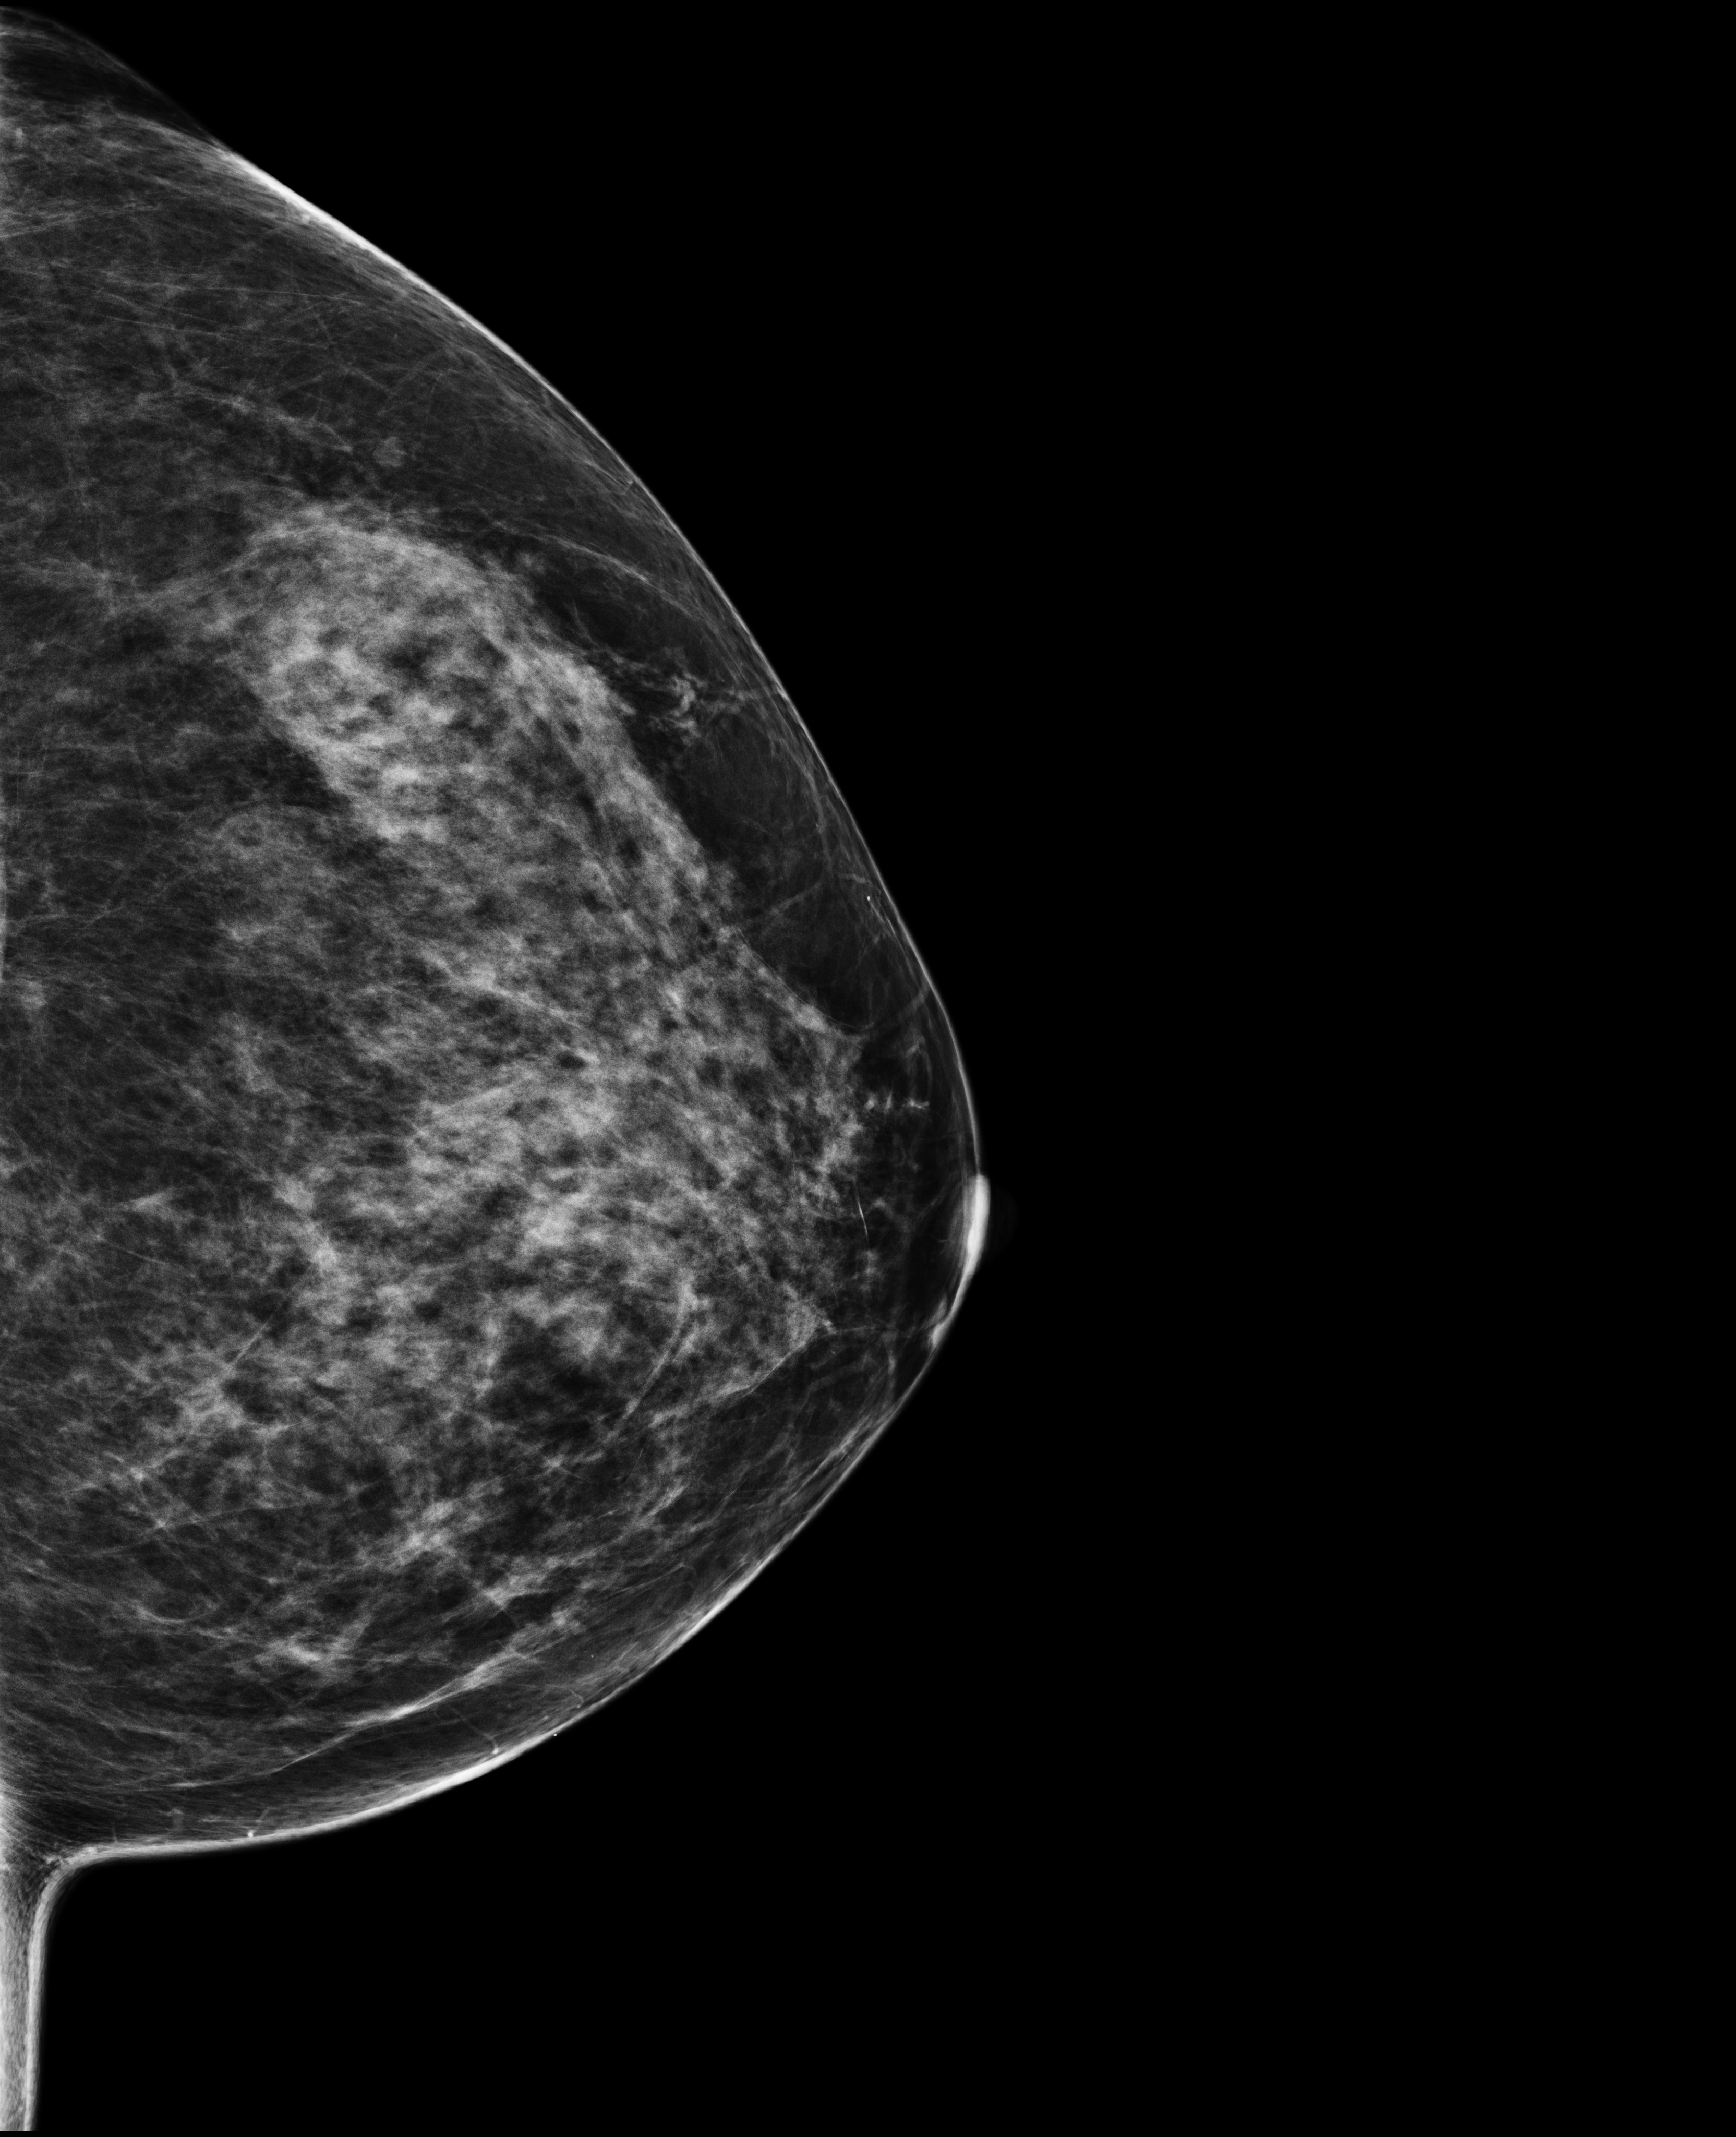
Annual screening mammography examination; compressed breast thickness 74 mm; system: Selenia Dimensions. Female patient, age 47 years.
Image type: full-field digital mammogram. Breast: left. Projection: CC view.